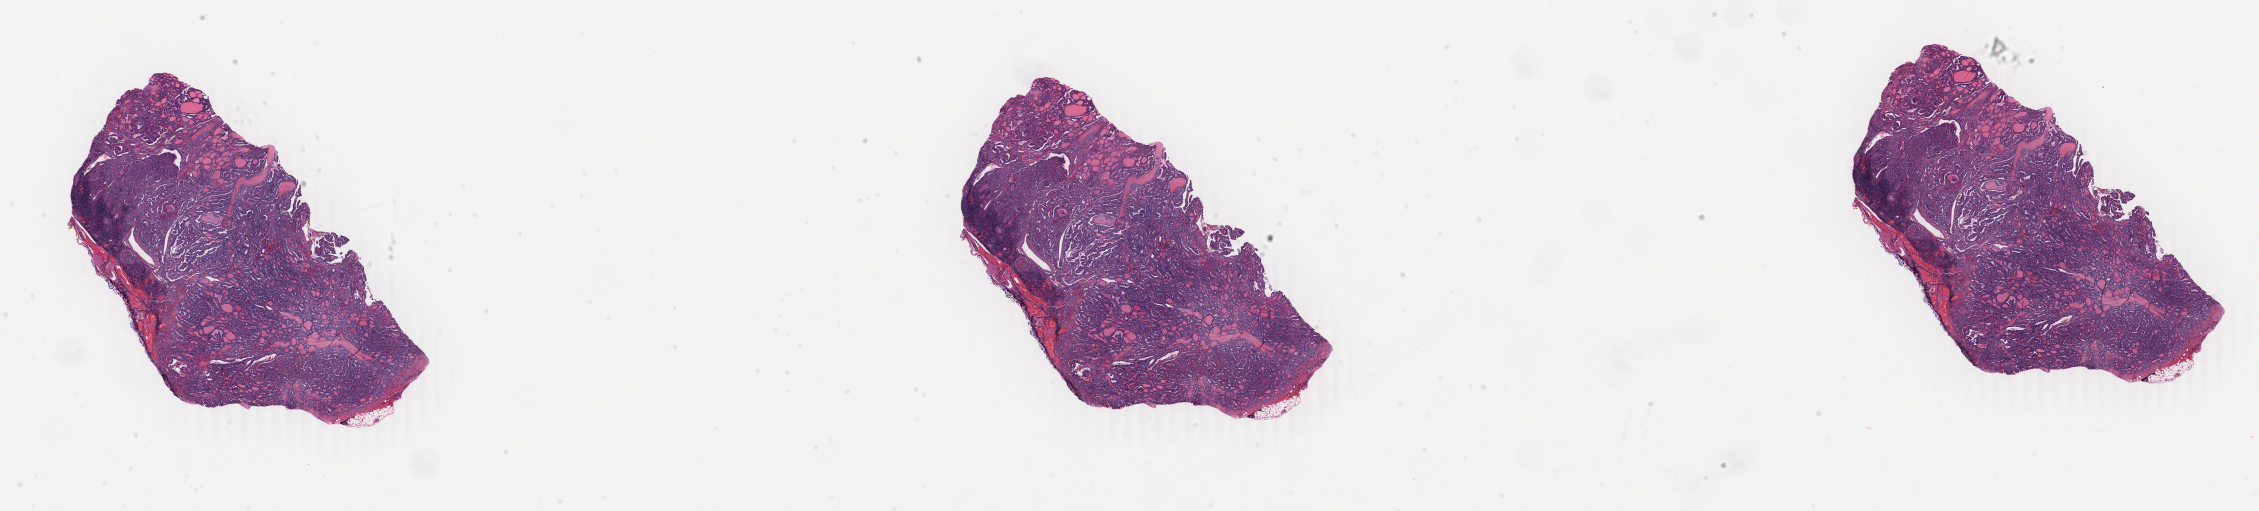
H&E whole-slide image — shown as a low-resolution overview of the whole scanned area (about 35.9 x 8.1 mm), formalin-fixed paraffin-embedded (FFPE) diagnostic section, thyroid, primary tumour sample. Female, age 65 years at initial diagnosis.
Histologic diagnosis: Papillary adenocarcinoma, NOS.